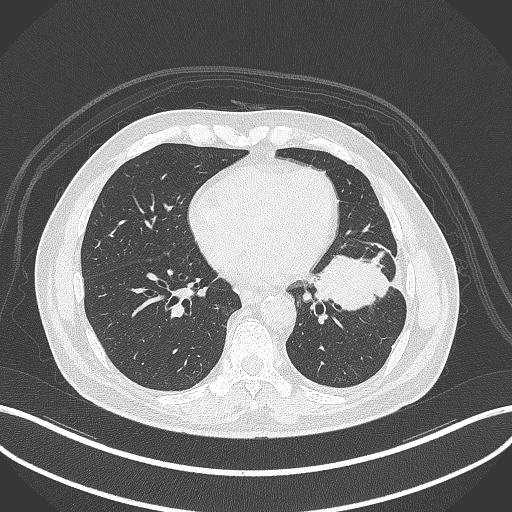
Chest CT, one axial slice; slice 139 of 230 in the series (ordered by position); reconstruction kernel B70f; lung window (W 1500 / L -600 HU); 1 mm slice thickness; 512 × 512 image matrix. Patient: male, 68 years. Case-level facts recorded for this patient, not image findings: clinical TNM (as recorded): T2b N0 M0.
Annotated regions visible in this slice (rectangle marked by the reading radiologist):
- lung tumour (recorded histology: squamous cell carcinoma): bounding box <315,256,395,315> (left, top, right, bottom; pixels)